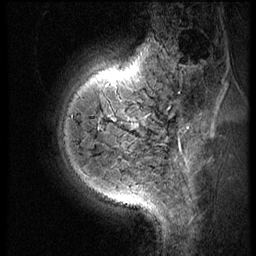
Breast MRI (dynamic contrast-enhanced), one sagittal slice. Position 14 of 60 along the scan axis. 3 images stored at this slice position (order not interpretable as contrast timing). 1.5 T. TE 4.2 ms, TR 9 ms. 256 × 256 image matrix, field of view 180 × 180 mm. Patient: female, 38 years. Case-level facts recorded for this patient, not image findings: setting: breast cancer imaged before/during neoadjuvant chemotherapy; receptor status: triple-negative.
Structures marked on this image (semi-automatically segmented with operator editing):
- analysis volume of interest (the breast-tissue region the enhancement analysis was run in; not a lesion): bounding box (x1, y1, x2, y2) in pixels: (119, 93, 165, 150)
- tumour enhancement mask (voxels above the 140 % enhancement threshold inside the analysis volume of interest): (128, 121, 140, 132)